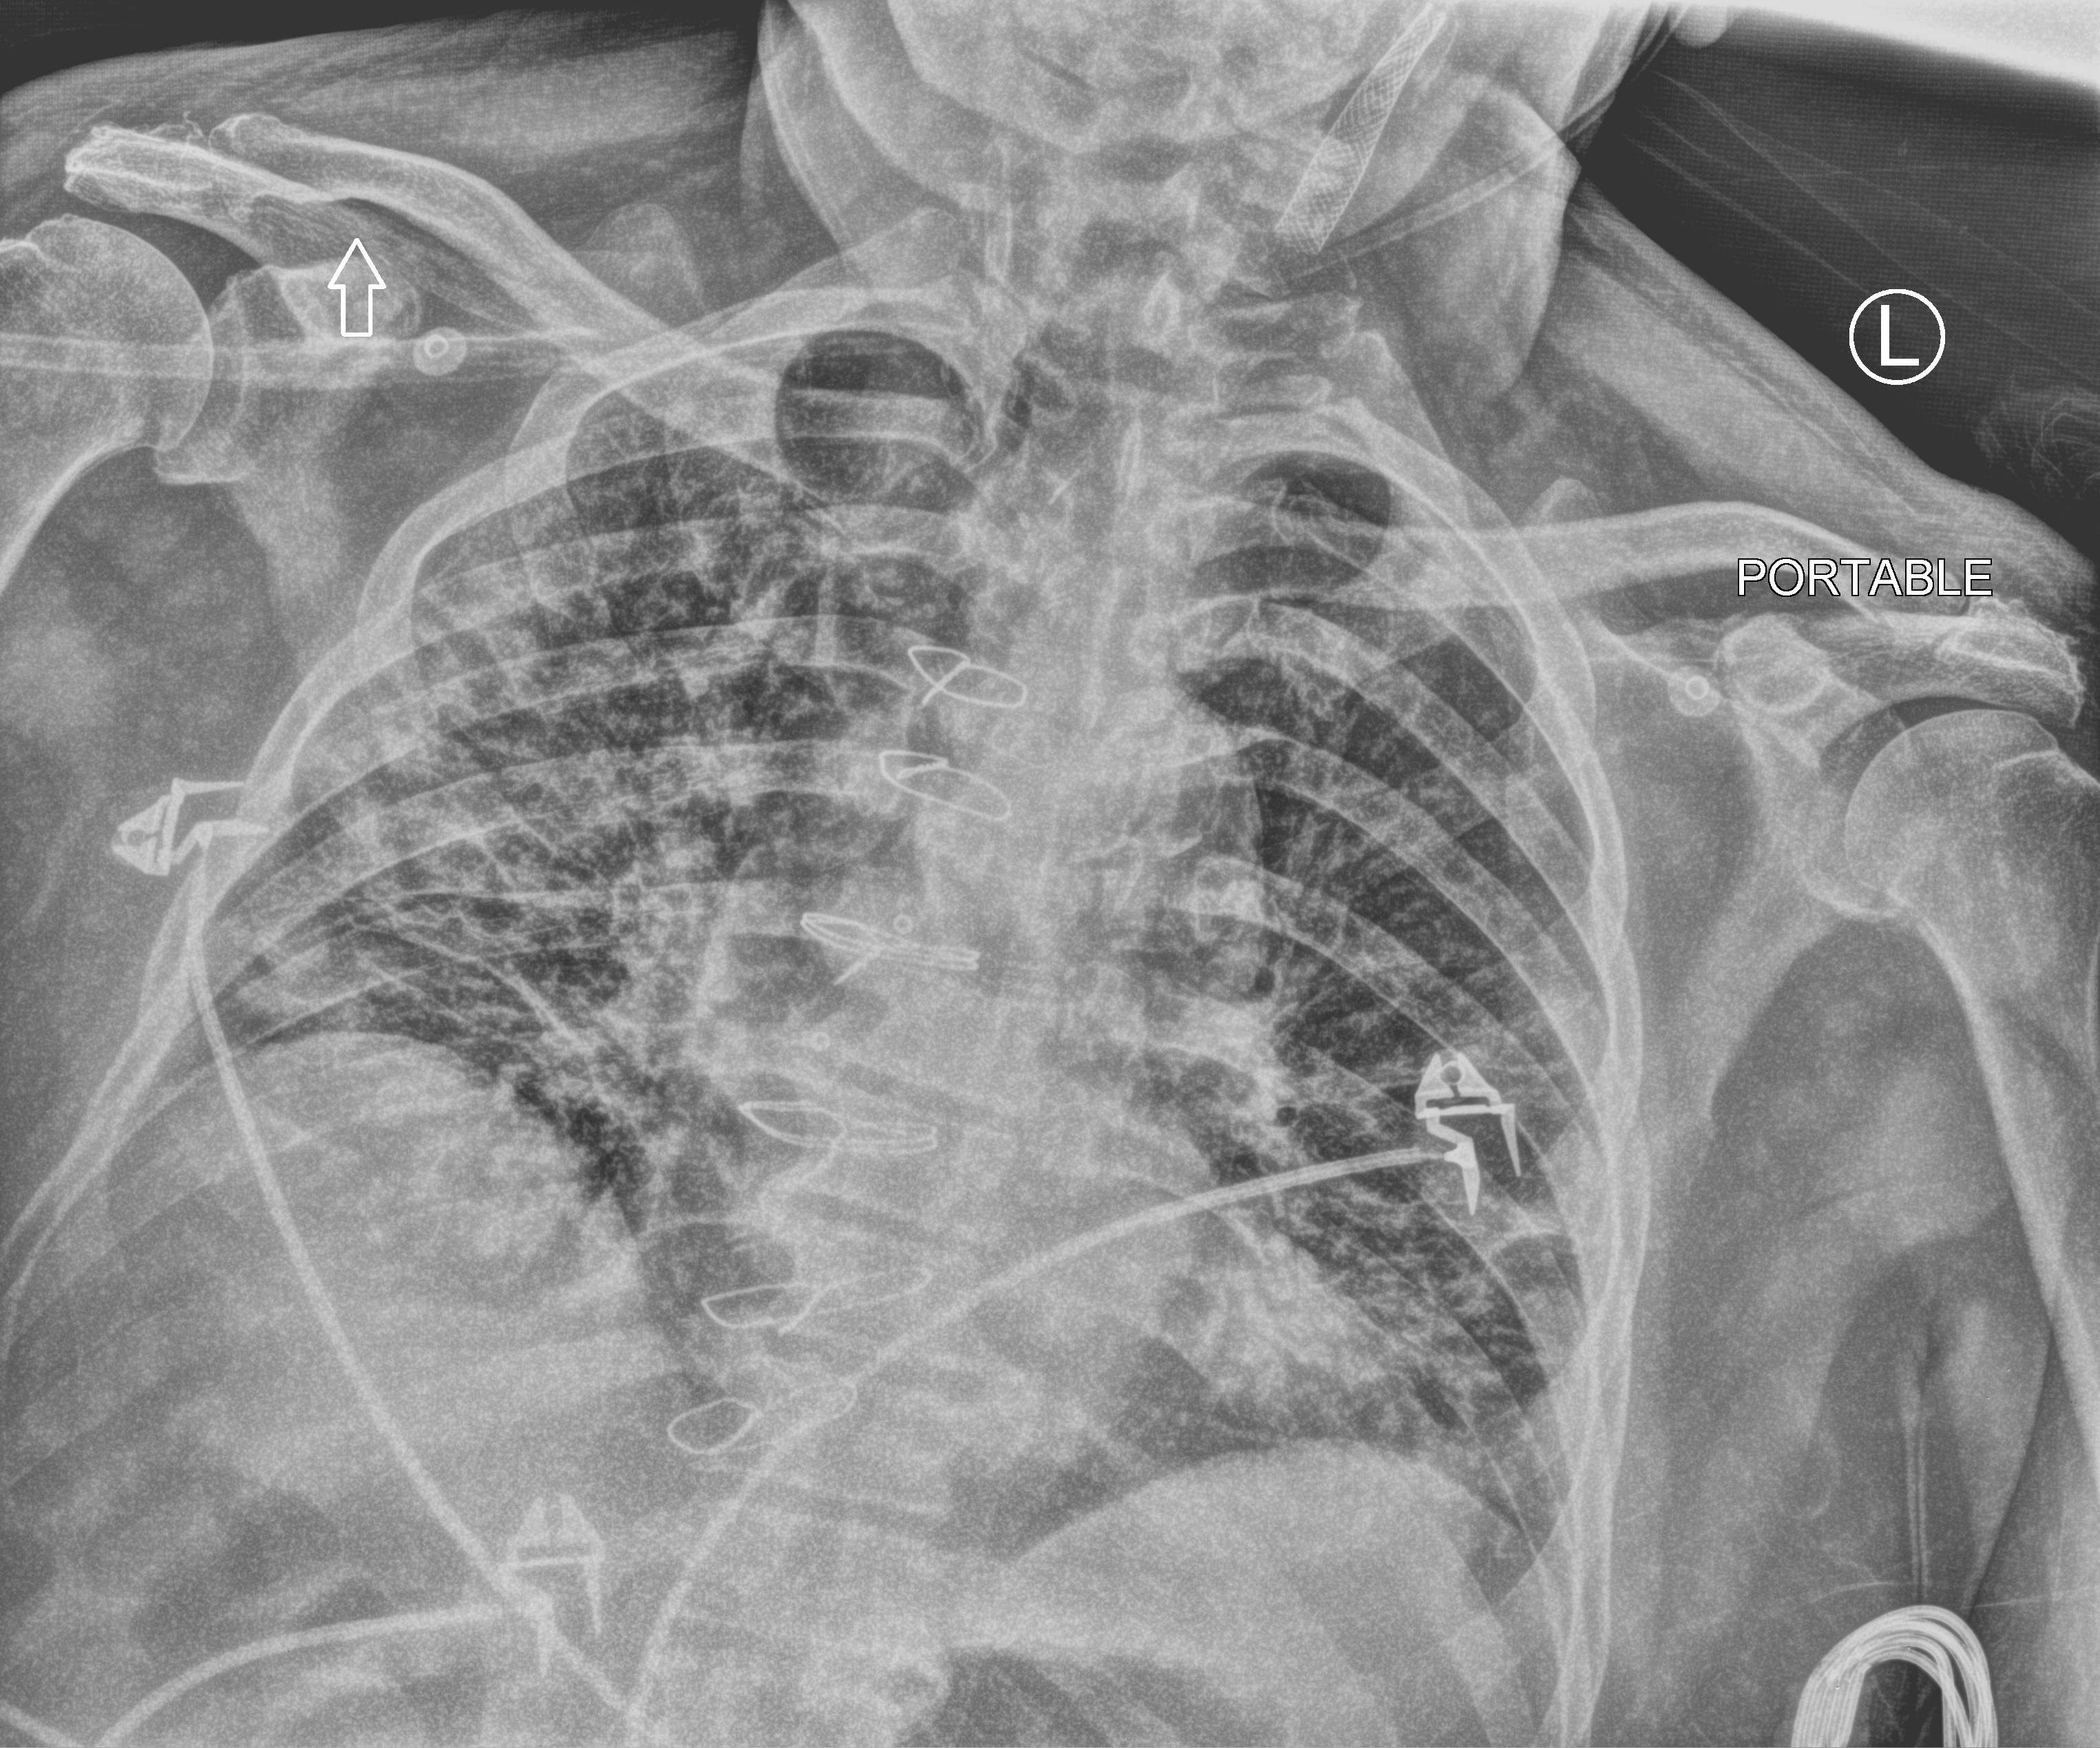
Bedside chest radiograph (computed radiography), anteroposterior (AP) projection. Patient hospitalised with COVID-19; male, aged 75–90 years.
Admission-level facts for this patient (not findings on this image; timing relative to this image not recorded): smoking status (admission record): never; length of hospital stay: 9 days; hypertension (admission record): yes.